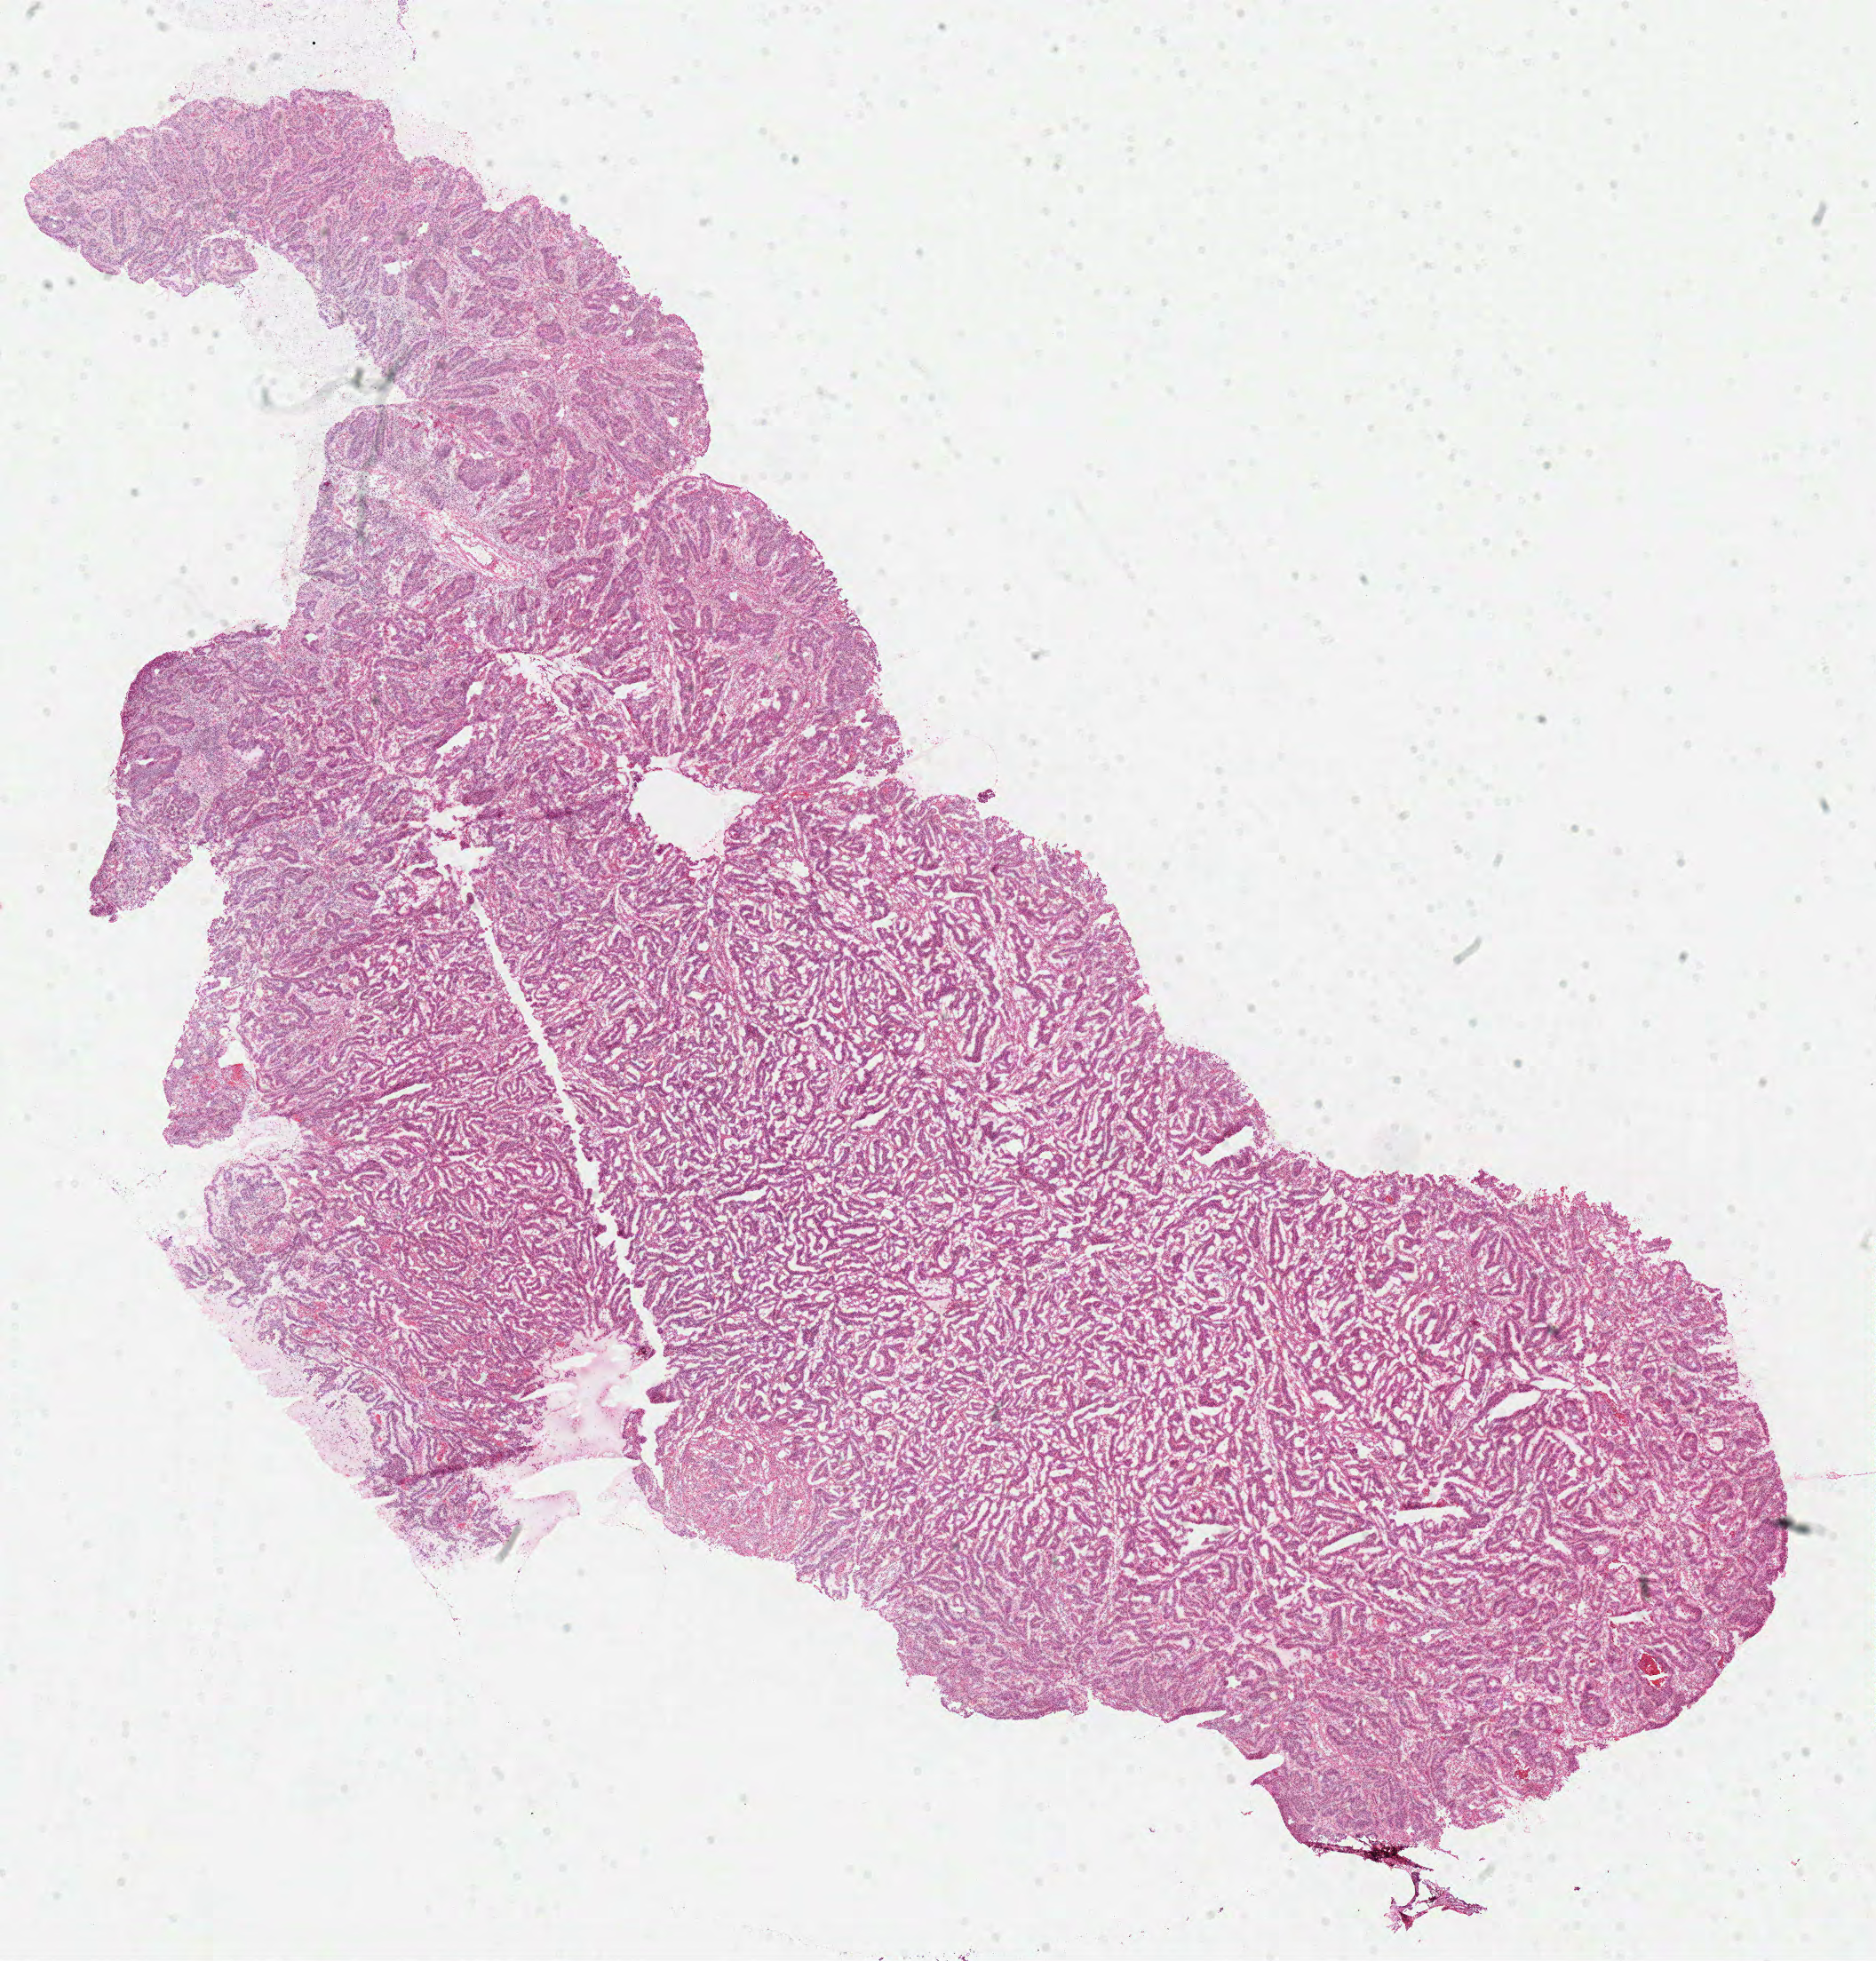
Whole-slide histology image, H&E, shown as a low-resolution overview of the whole scanned area (about 16.6 x 17.4 mm, acquisition: 40x scan). Frozen section from the top of the tissue portion. Primary tumour sample from the rectum. Patient: female, age at initial diagnosis 31 years. Composition of this section per pathologist review: tumour cells 83%, tumour nuclei 75%, normal cells 2%, stromal cells 10%, necrosis 5%. Inflammatory infiltration, as recorded: lymphocyte infiltration 20%, monocyte infiltration 0%, neutrophil infiltration 0%.
TNM: T2 N1b M0. AJCC pathologic stage: IIIA. Diagnosis: Adenocarcinoma, NOS (rectosigmoid junction).